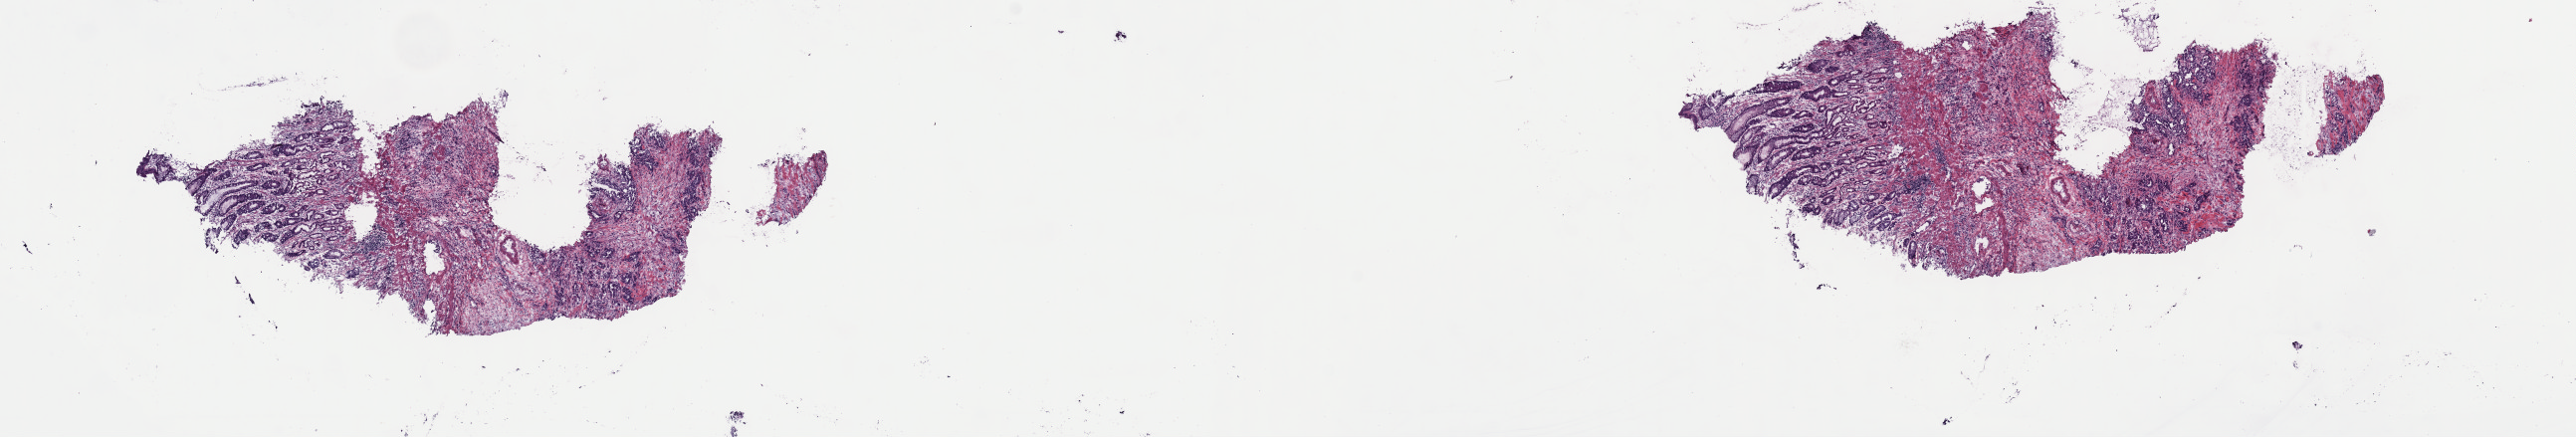
H&E whole-slide image, a low-resolution overview of the entire scanned area, about 20.4 x 3.5 mm (from a 40x scan), frozen section from the top of the tissue portion, stomach, primary tumour sample. Male patient; age at initial diagnosis 74 years. Histologic grade: G3 (poorly differentiated). Slide review estimates, as recorded: tumour cells 65%, tumour nuclei 65%, normal cells 8%, stromal cells 27%, necrosis 0%. Infiltration values recorded for this section: lymphocyte infiltration 5%, monocyte infiltration 1%, neutrophil infiltration 1%.
• lymph nodes positive (case pathology): 3 of 29 examined
• histologic diagnosis: Carcinoma, diffuse type (gastric antrum)
• AJCC pathologic stage: IIIB (7th edition)